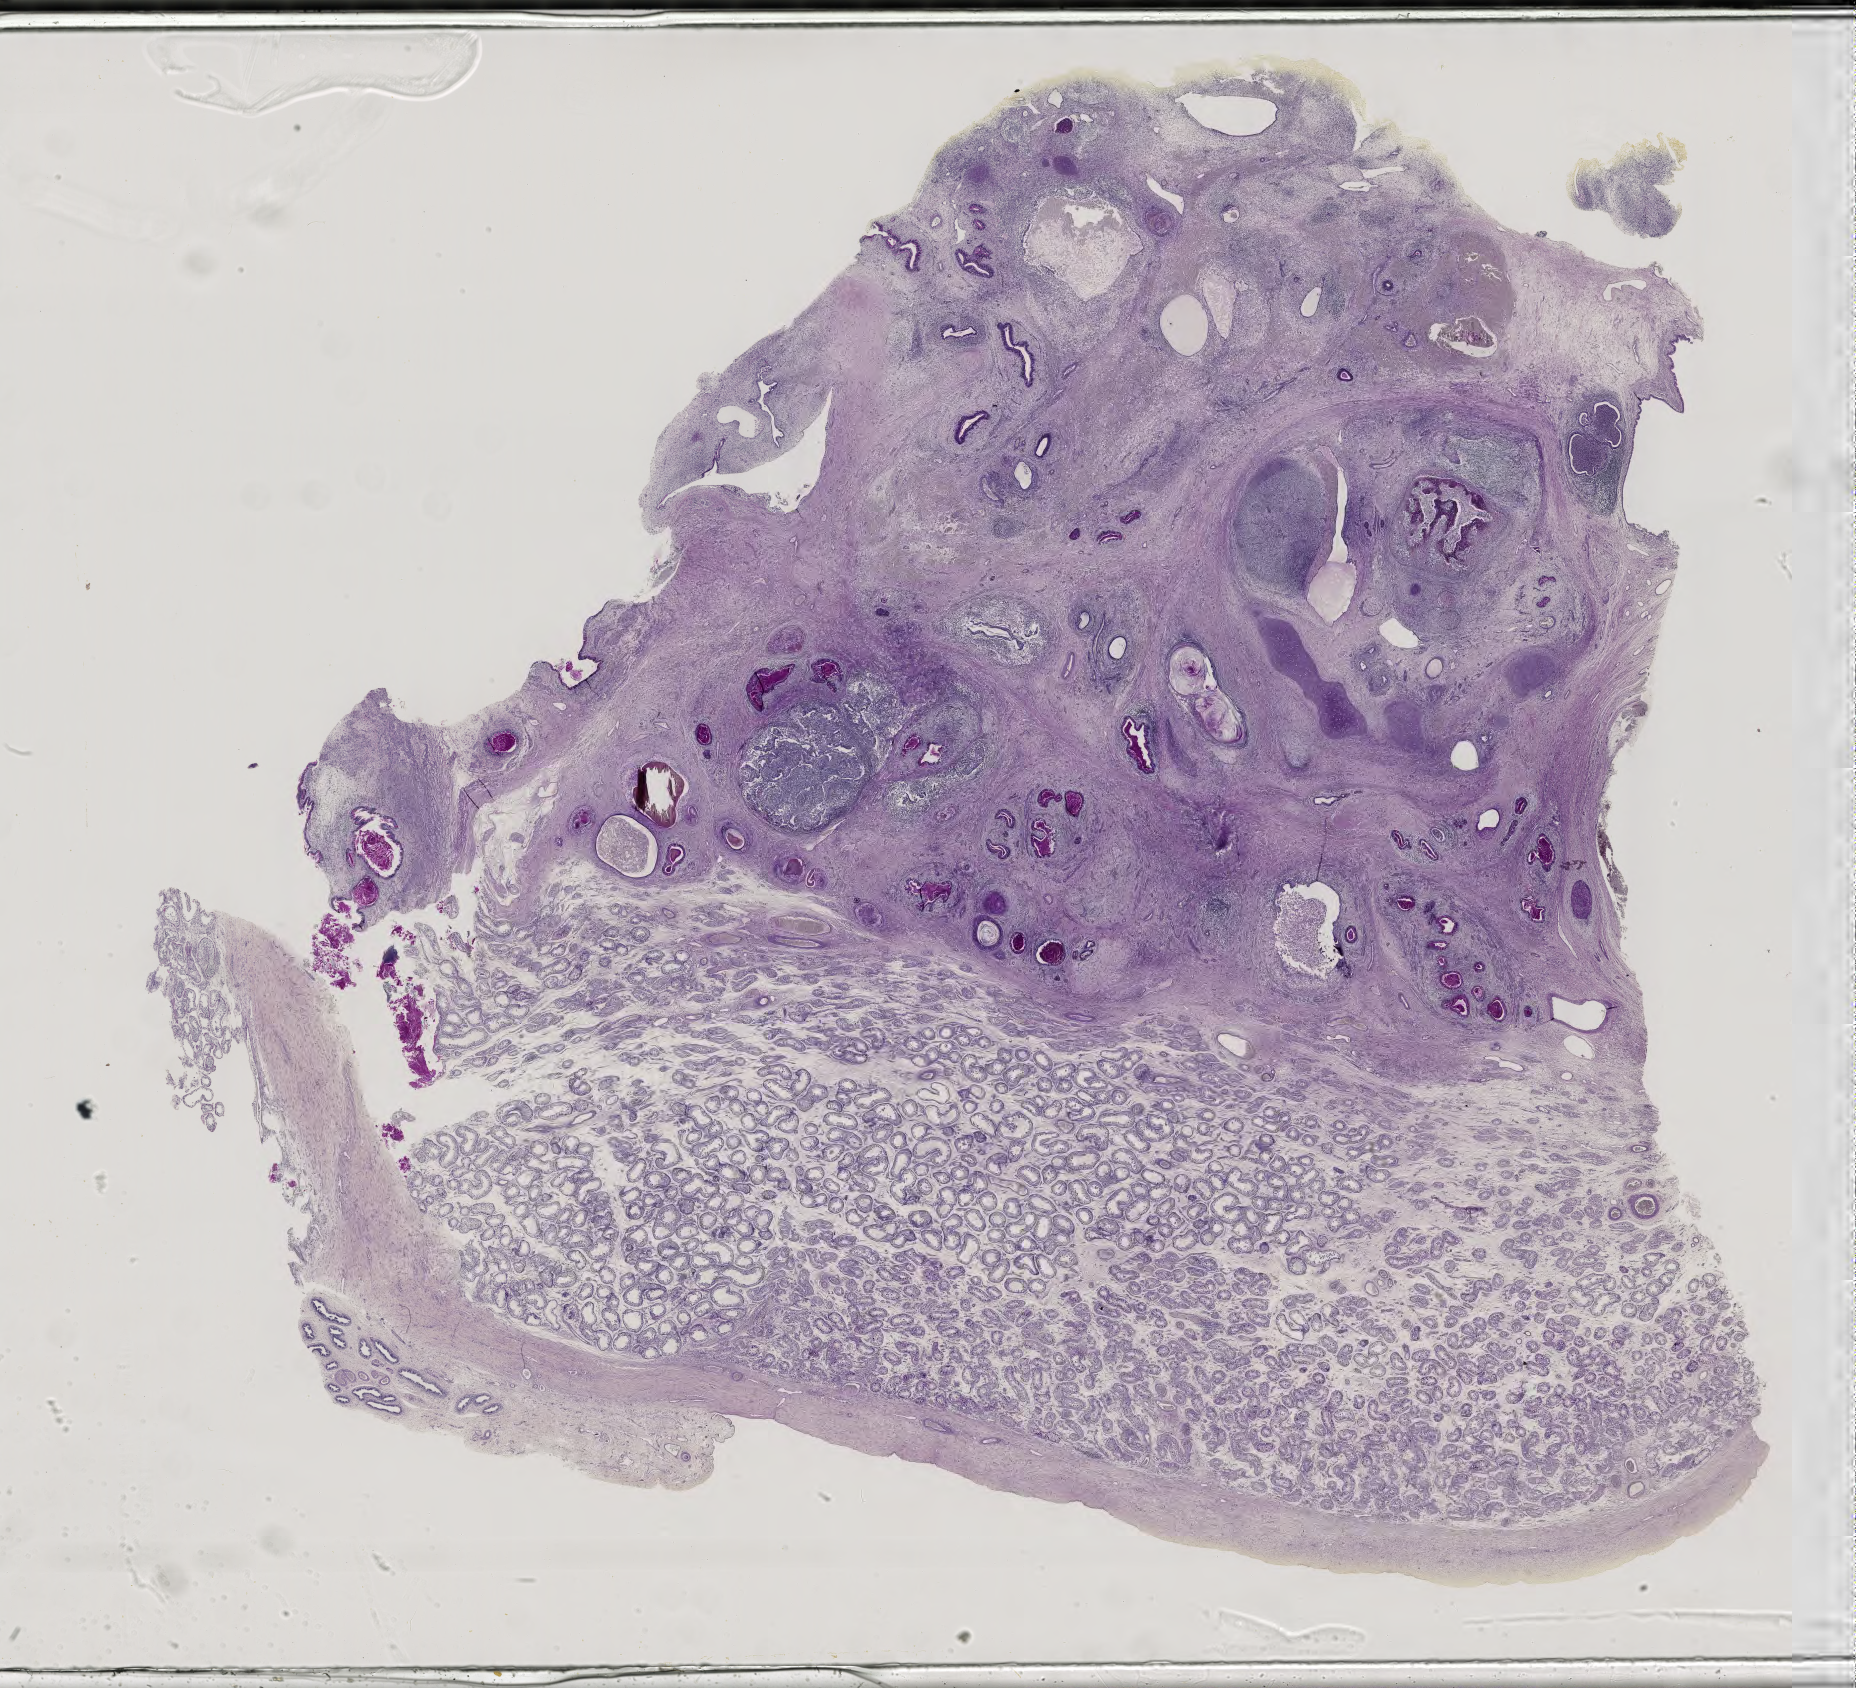
Digitized Hematoxylin and eosin (H&E) stained tissue section (whole slide), low-resolution overview of the scanned area, about 27.0 x 24.6 mm, formalin-fixed paraffin-embedded (FFPE) diagnostic section, sample: primary tumour, testis. Patient: male, age at initial diagnosis 28 years.
* AJCC pathologic stage: IS (5th edition)
* TNM: T1 N0 M0
* diagnosis: Teratoma, benign